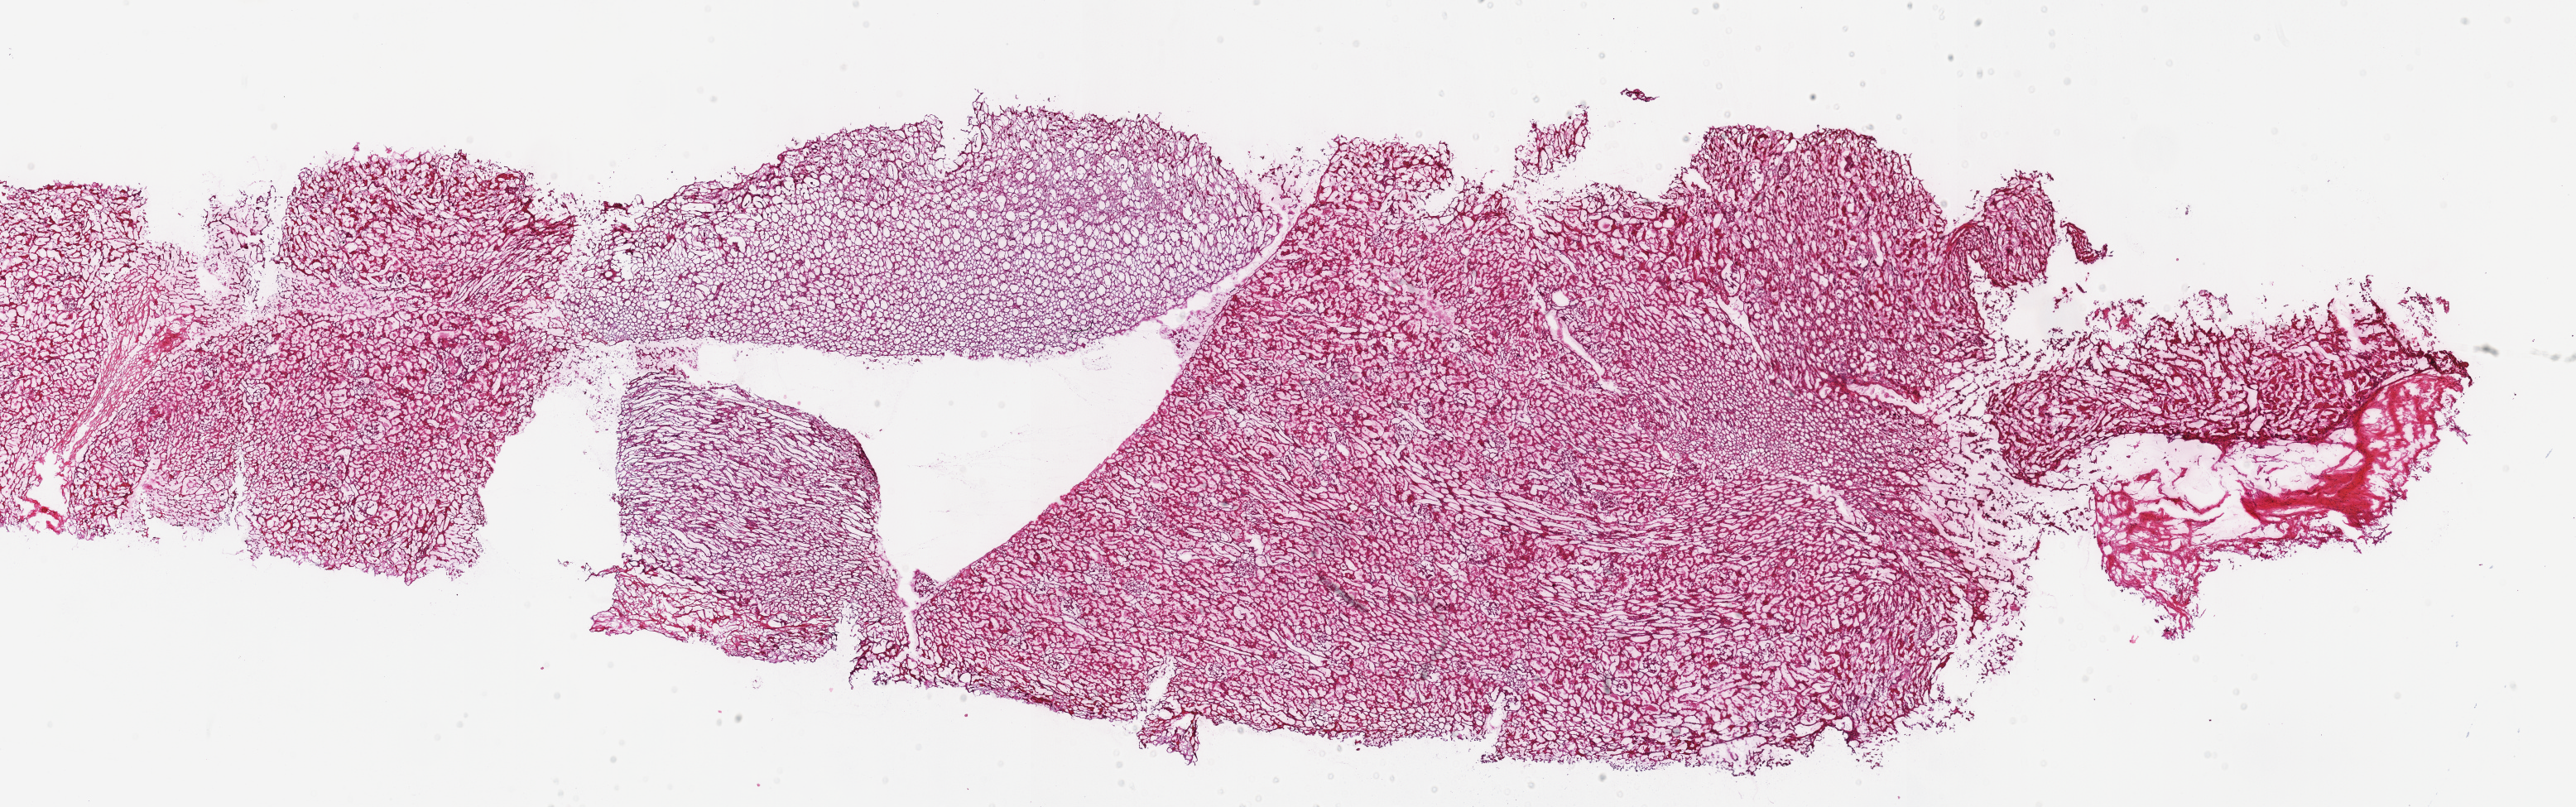
H&E-stained whole-slide image, whole scanned area (about 24.5 x 7.7 mm, acquisition: 40x scan) shown as a low-resolution overview, frozen section from the top of the tissue portion, solid tissue normal (non-tumour tissue) sample from the kidney. Patient: female, age at initial diagnosis 17 years.
This section: solid tissue normal (non-tumour) sample from the same patient. Patient diagnosis: Renal cell carcinoma, chromophobe type.